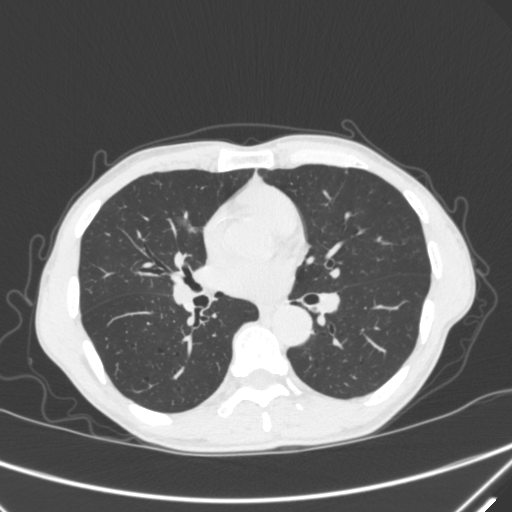
Chest CT, one axial slice. Slice 174 of 340 in the series (ordered by position). Lung window (W 1500 / L -600 HU). 512 × 512 image matrix, field of view 350 × 350 mm. Male patient, age 67 years. From the clinical record (not read from this slice): clinical TNM (as recorded): T1c N0 M0; histopathological grade: G1-2.
Annotated regions visible in this slice (rectangle marked by the reading radiologist):
- lung tumour (recorded histology: adenocarcinoma): box from (x=172, y=212) to (x=201, y=245) px